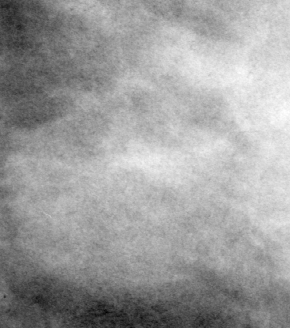
Crop from a digitized film mammogram around one marked abnormality; left breast; CC view; BI-RADS breast density category 3 (scale 1–4).
- Mass, shape oval, margins microlobulated; BI-RADS assessment category 4; pathology (as recorded): malignant.